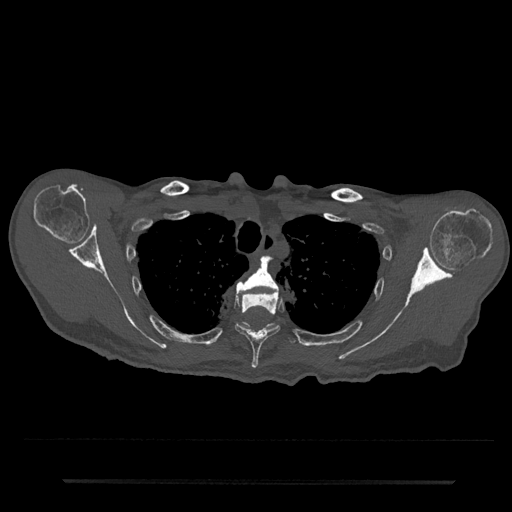
CT including the spine, one axial slice. Position 621 of 797 along the scan axis. Reconstruction kernel Br40s/3. 120 kVp. Bone window (W 1800 / L 400 HU). 0.5 mm slice thickness. 512 × 512 image matrix. Male patient, age 74 years. Case-level facts recorded for this patient, not image findings: primary cancer: prostate.
Structures marked on this image (semi-automatically segmented with operator editing):
- T3 vertebra: bounding box <236,258,279,294> (left, top, right, bottom; pixels)
- T4 vertebra: <235,292,280,368>
- T5 vertebra: <241,322,296,344>